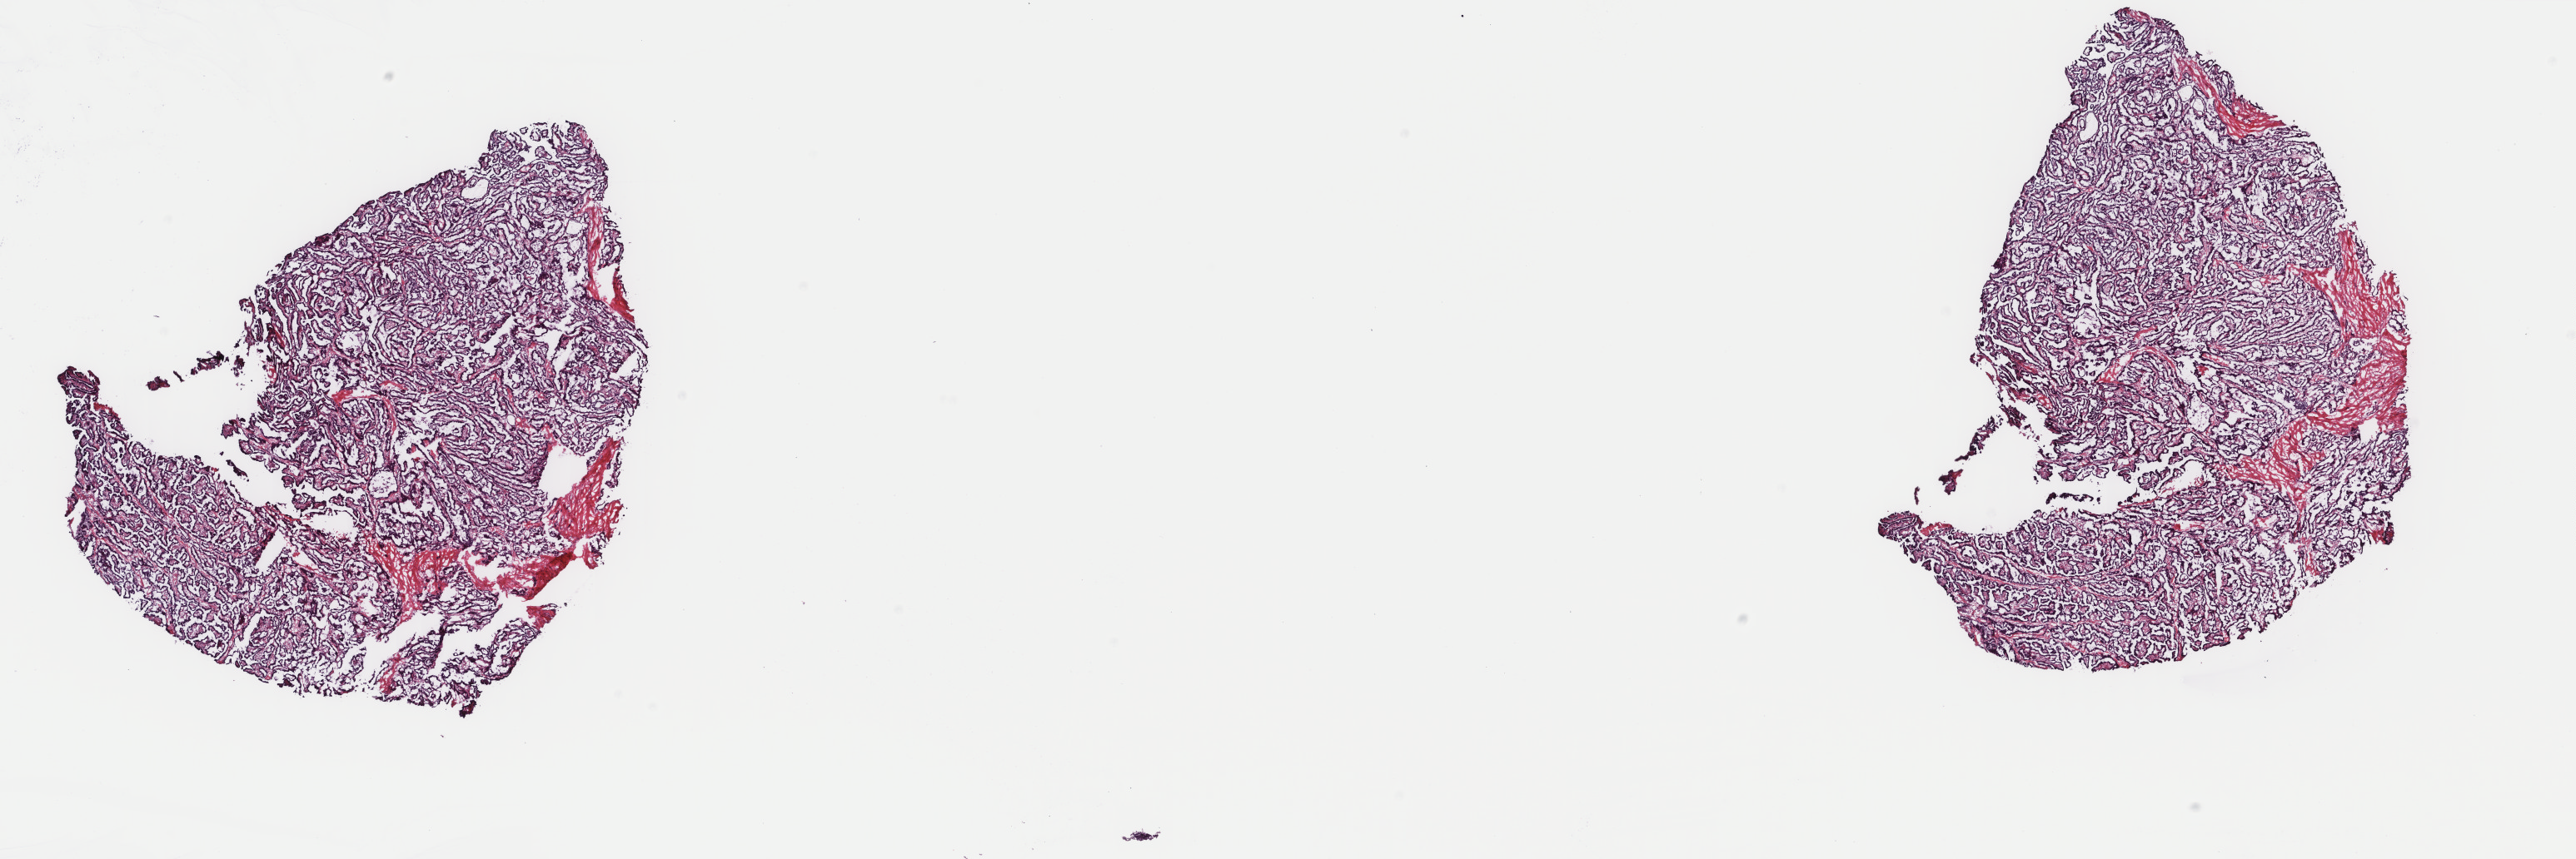
Digitized H&E tissue section (whole slide) — low-resolution overview of the scanned area, about 24.6 x 8.2 mm (from a 40x scan); frozen section from the top of the tissue portion; primary tumour sample from the thyroid. Female, age 34 years at initial diagnosis. Pathologist review of this section (percent, as recorded): tumour cells 90%, tumour nuclei 100%, normal cells 0%, stromal cells 10%, necrosis 0%. Infiltration values recorded for this section: lymphocyte infiltration 1%, monocyte infiltration 2%, neutrophil infiltration 0%.
• AJCC pathologic stage: I (6th edition)
• diagnosis: Papillary adenocarcinoma, NOS (thyroid gland)
• laterality: left